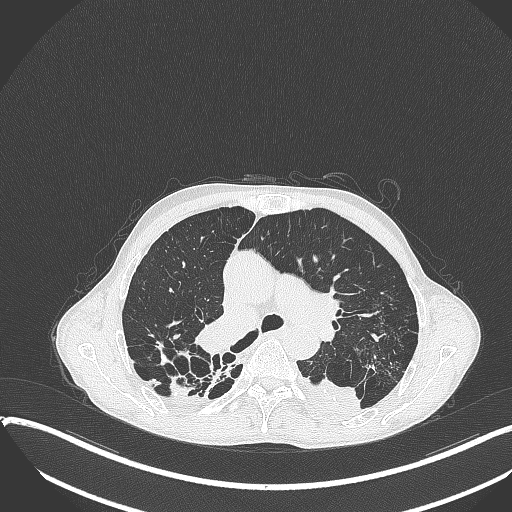
Chest CT, one axial slice; slice 248 of 401 in the series (ordered by position); reconstruction kernel B70f; 120 kVp; lung window (W 1500 / L -600 HU); 1 mm slice thickness; 512 × 512 image matrix, field of view 400 × 400 mm. Male patient, age 57 years. From the clinical record (not read from this slice): clinical TNM (as recorded): T4 N0 M0.
Outlined on this slice (rectangle marked by the reading radiologist):
- lung tumour (recorded histology: squamous cell carcinoma): bounding box [x1, y1, x2, y2] px = [300, 373, 363, 418]